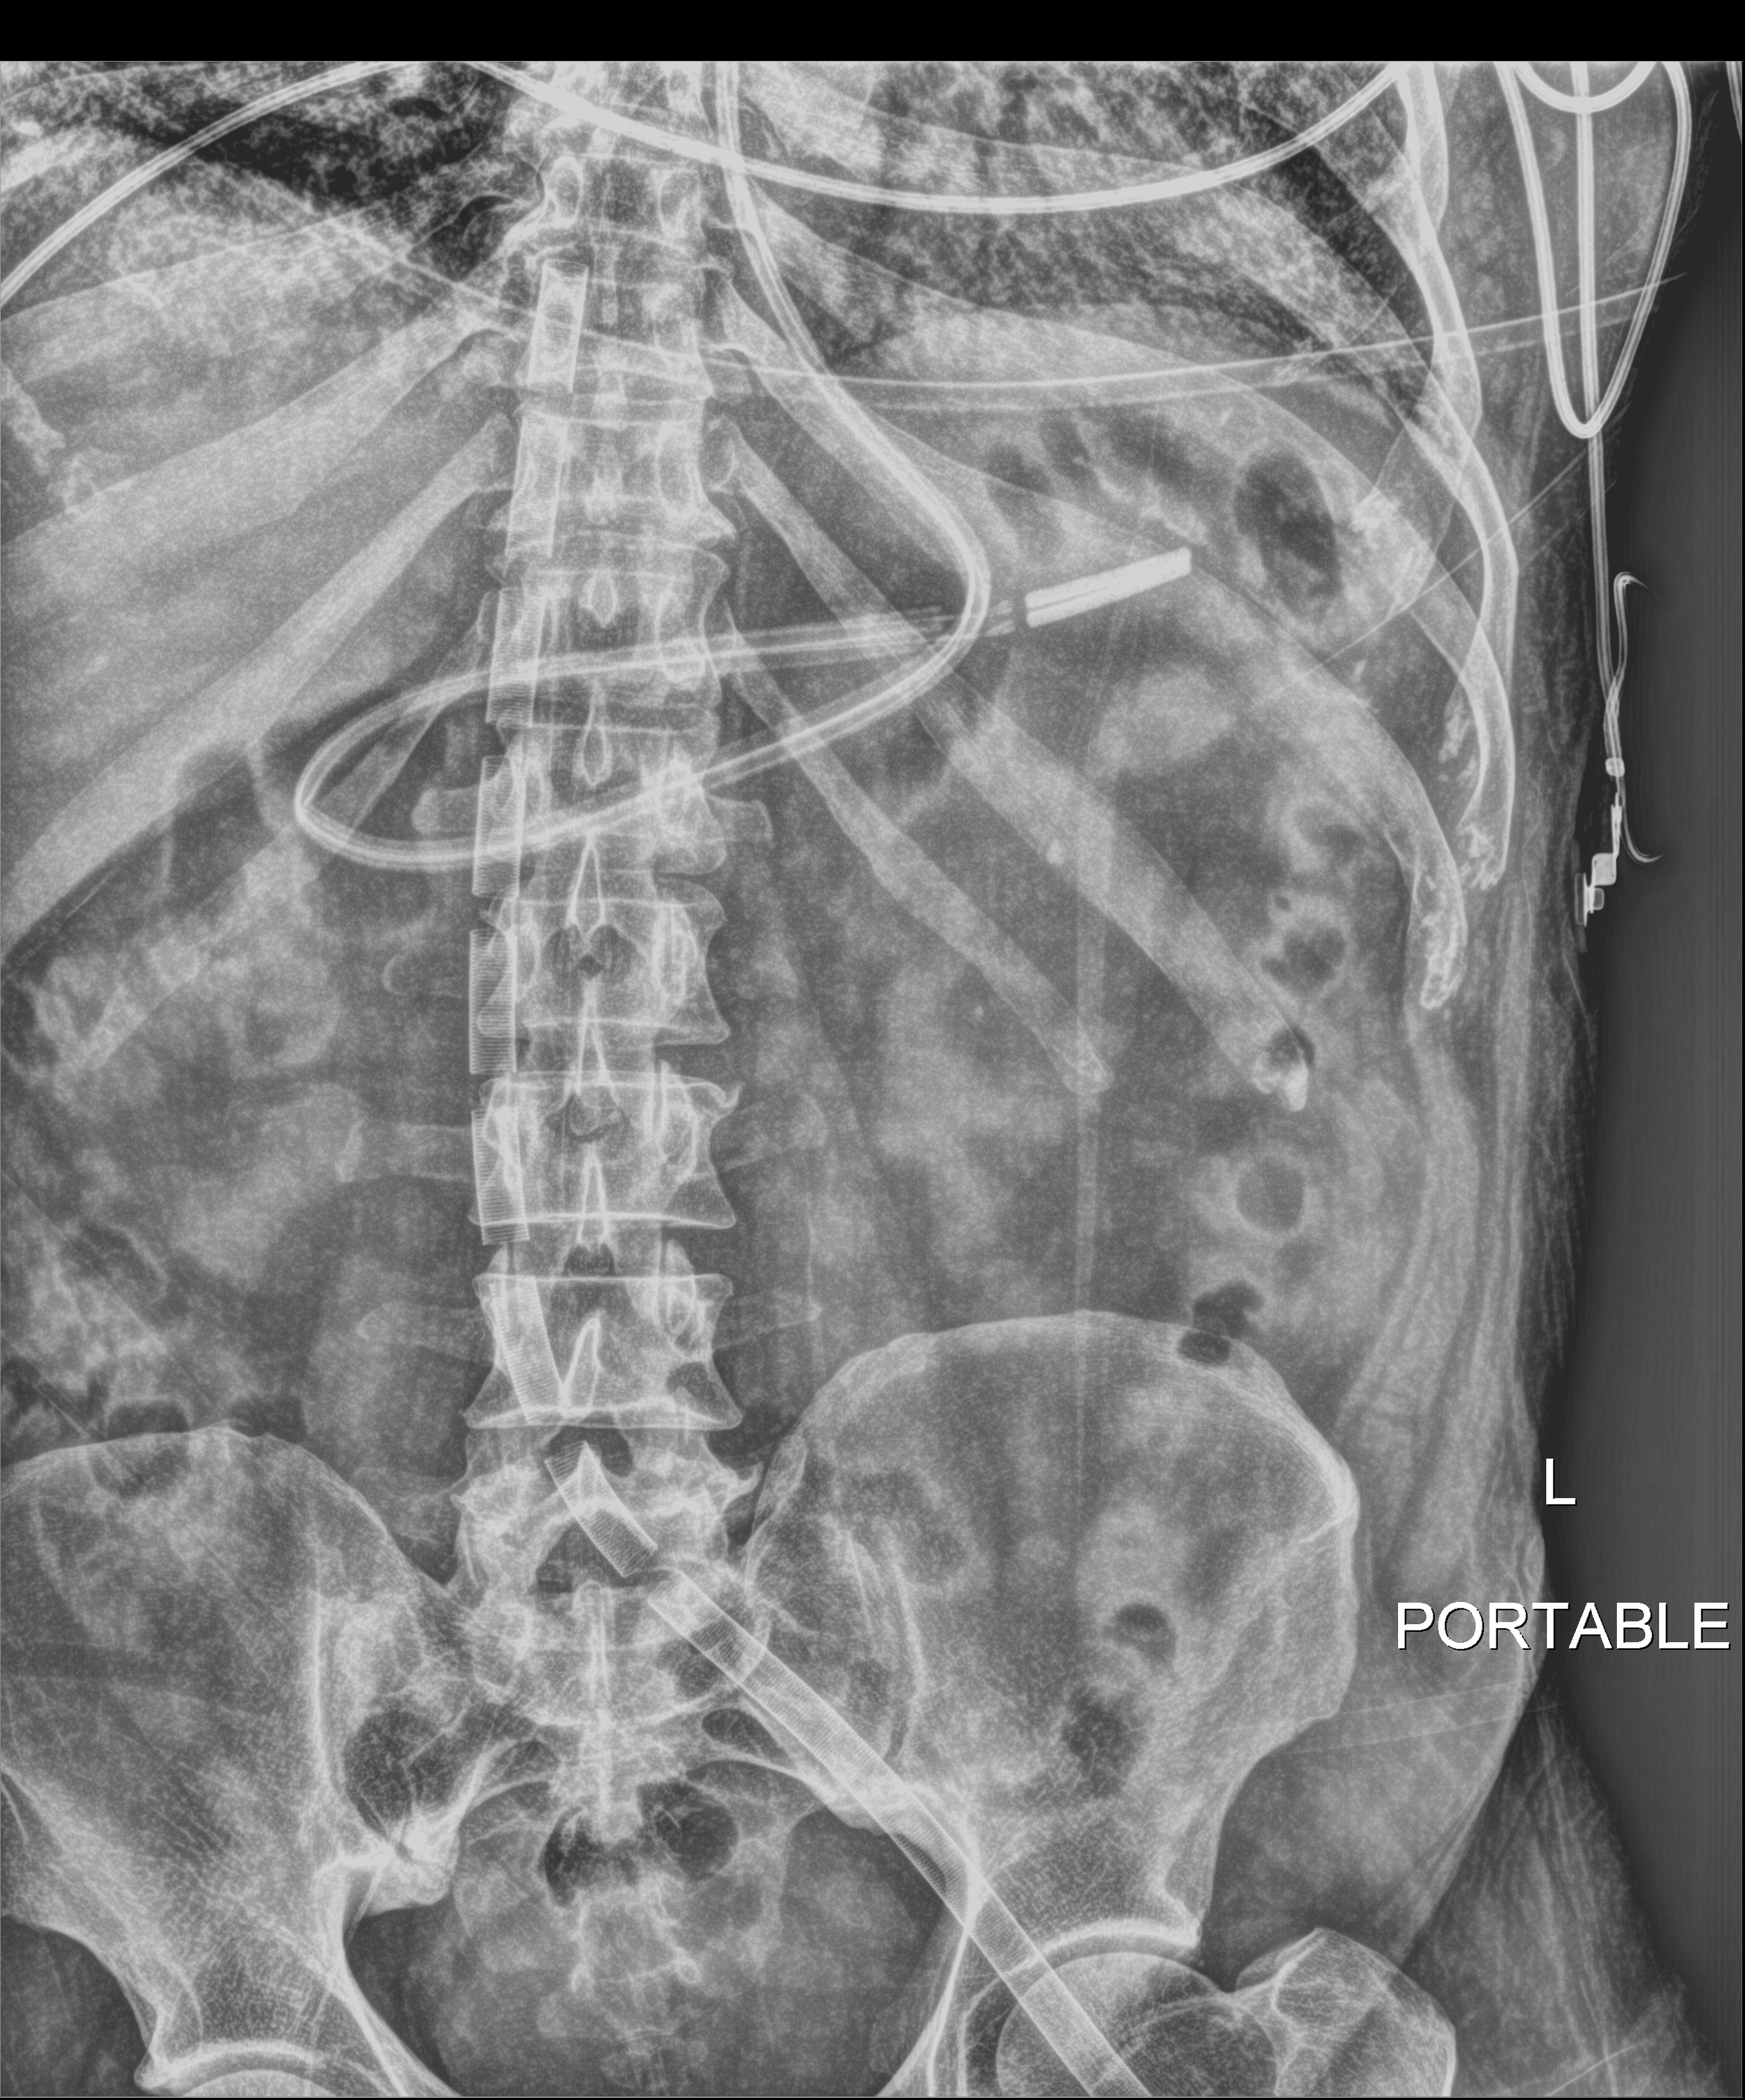
Abdomen X-ray (portable); anteroposterior (AP) projection. Male patient hospitalised with COVID-19, age 18–59 years.
From the hospital-stay record, not from the radiograph (when in the stay this image was taken is not recorded): mechanically ventilated during this hospital stay: yes; COPD (admission record): no; admitted to intensive care during this hospital stay: yes.